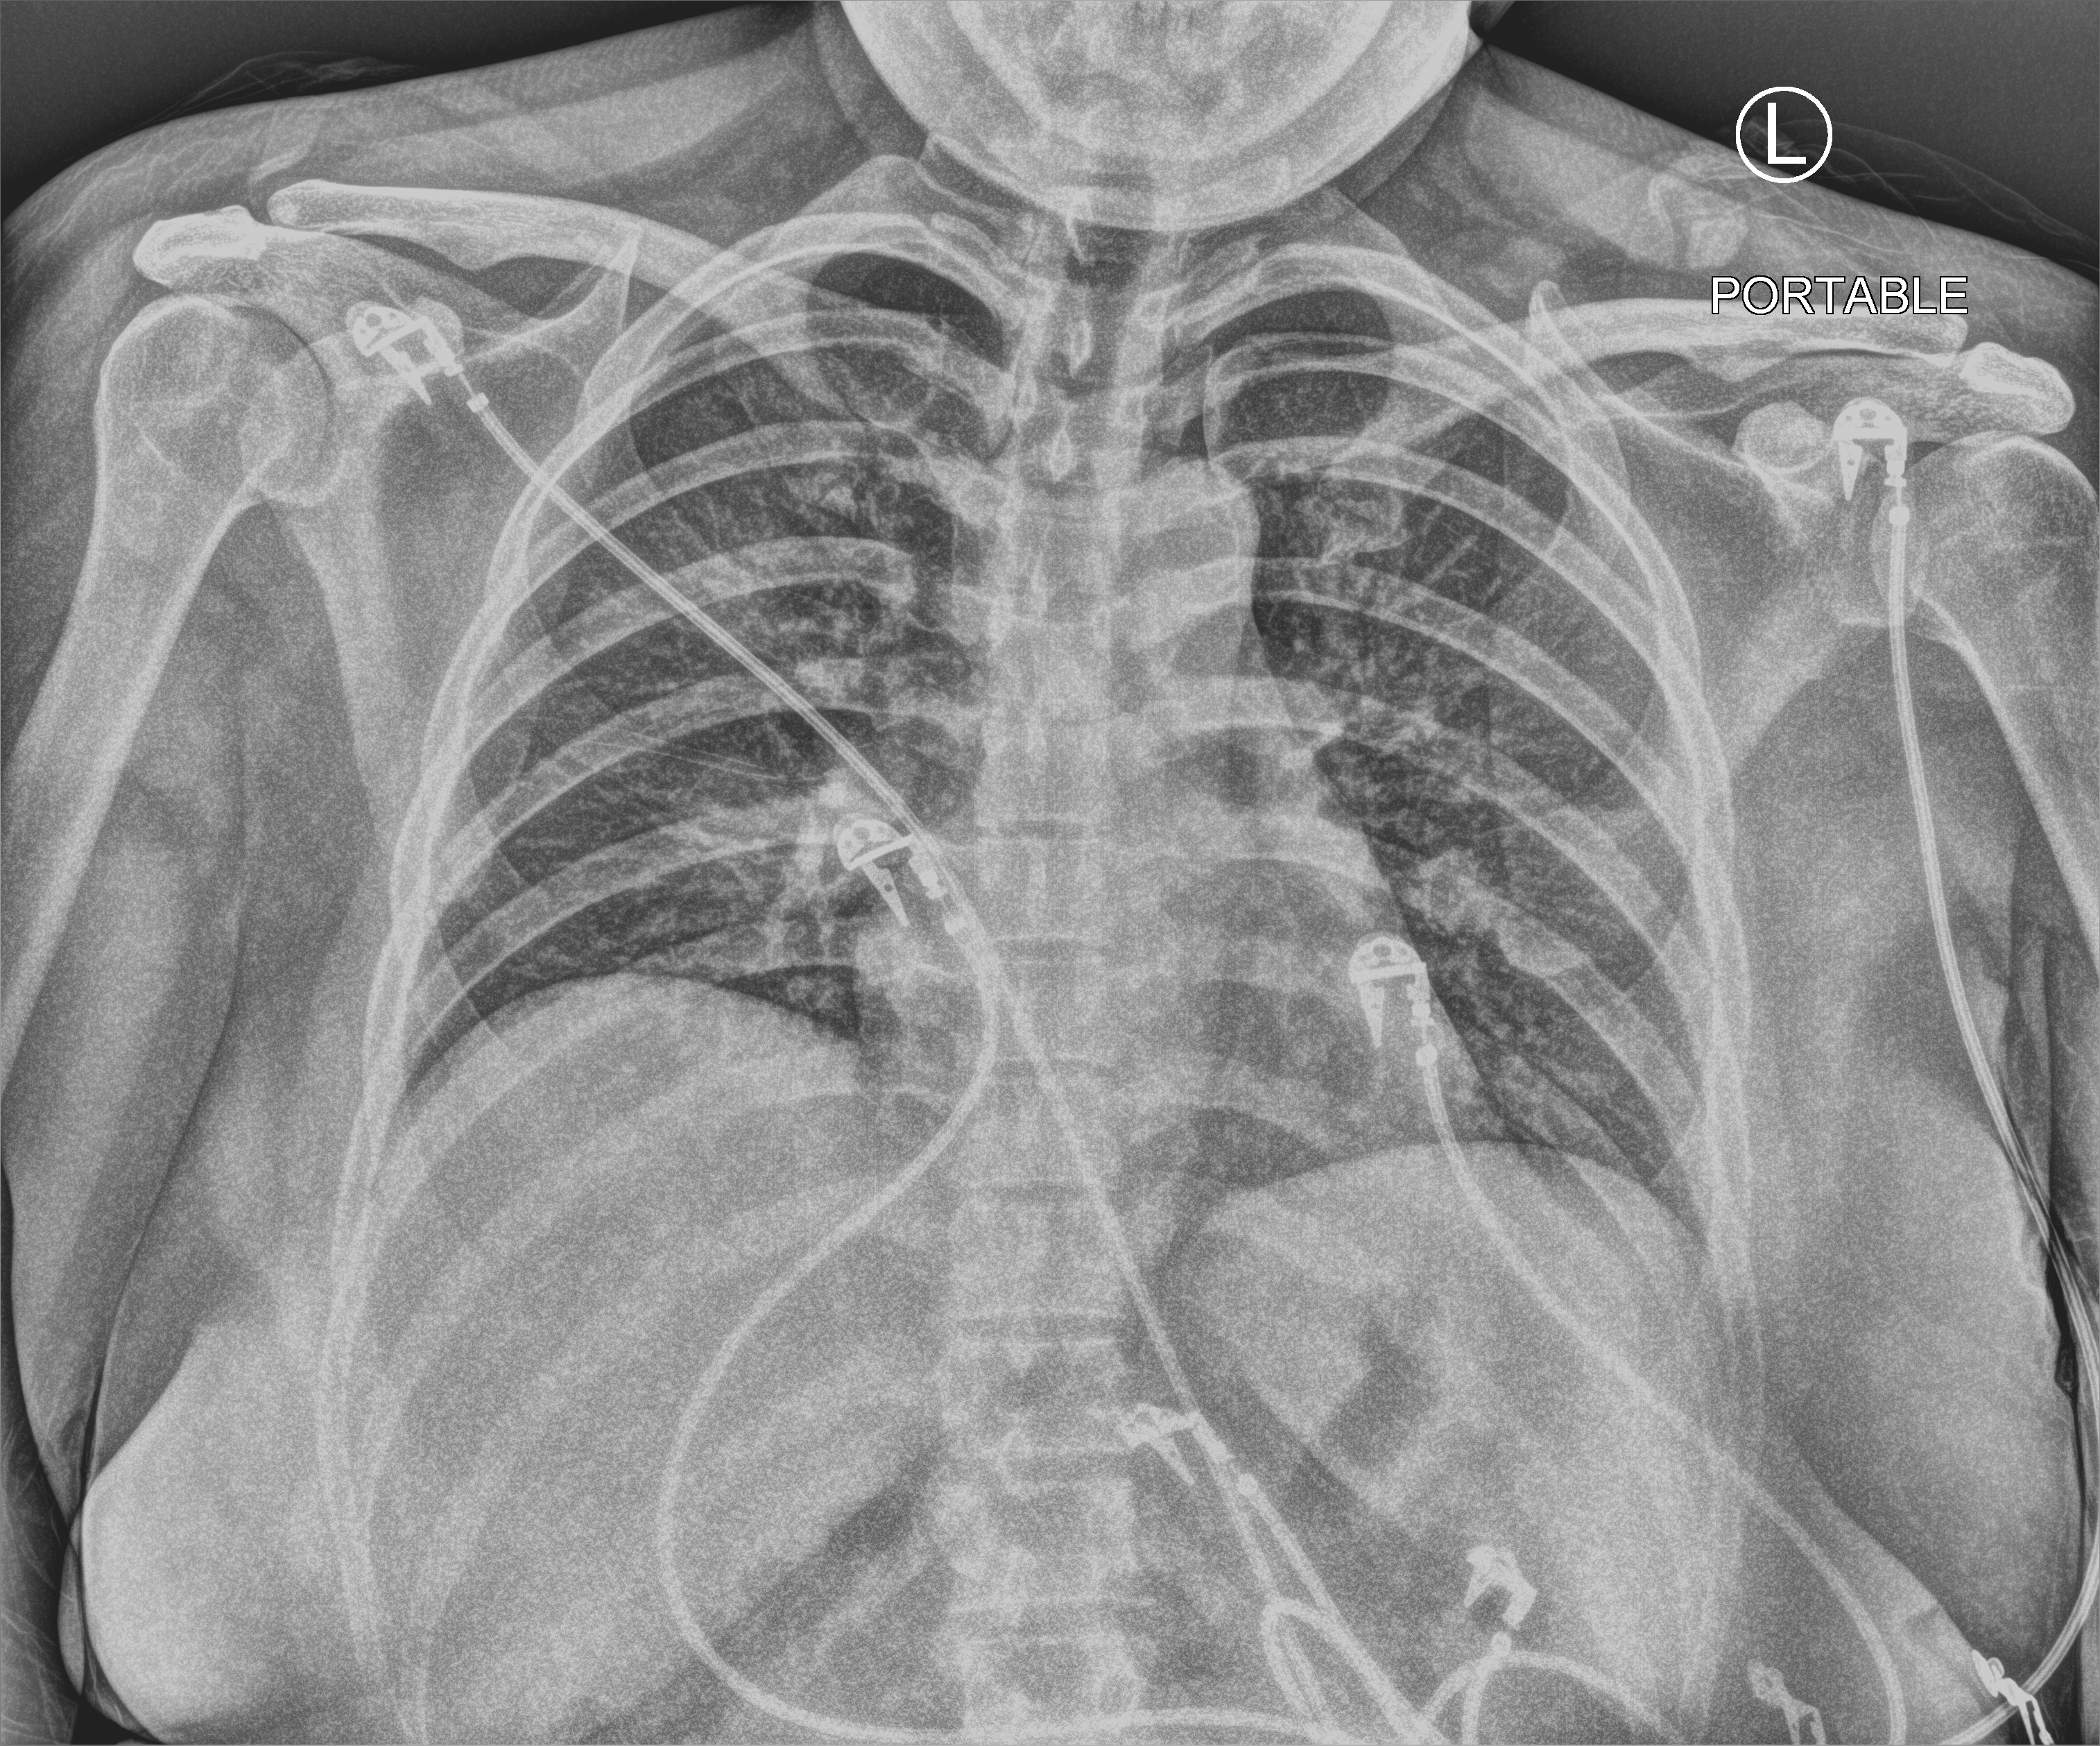
Bedside chest radiograph (computed radiography). Female patient hospitalised with COVID-19, age 18–59 years.
Hospital-stay facts (about this admission, not read from this image; timing relative to this image not recorded):
- diabetes (admission record): no
- admitted to intensive care during this hospital stay: no